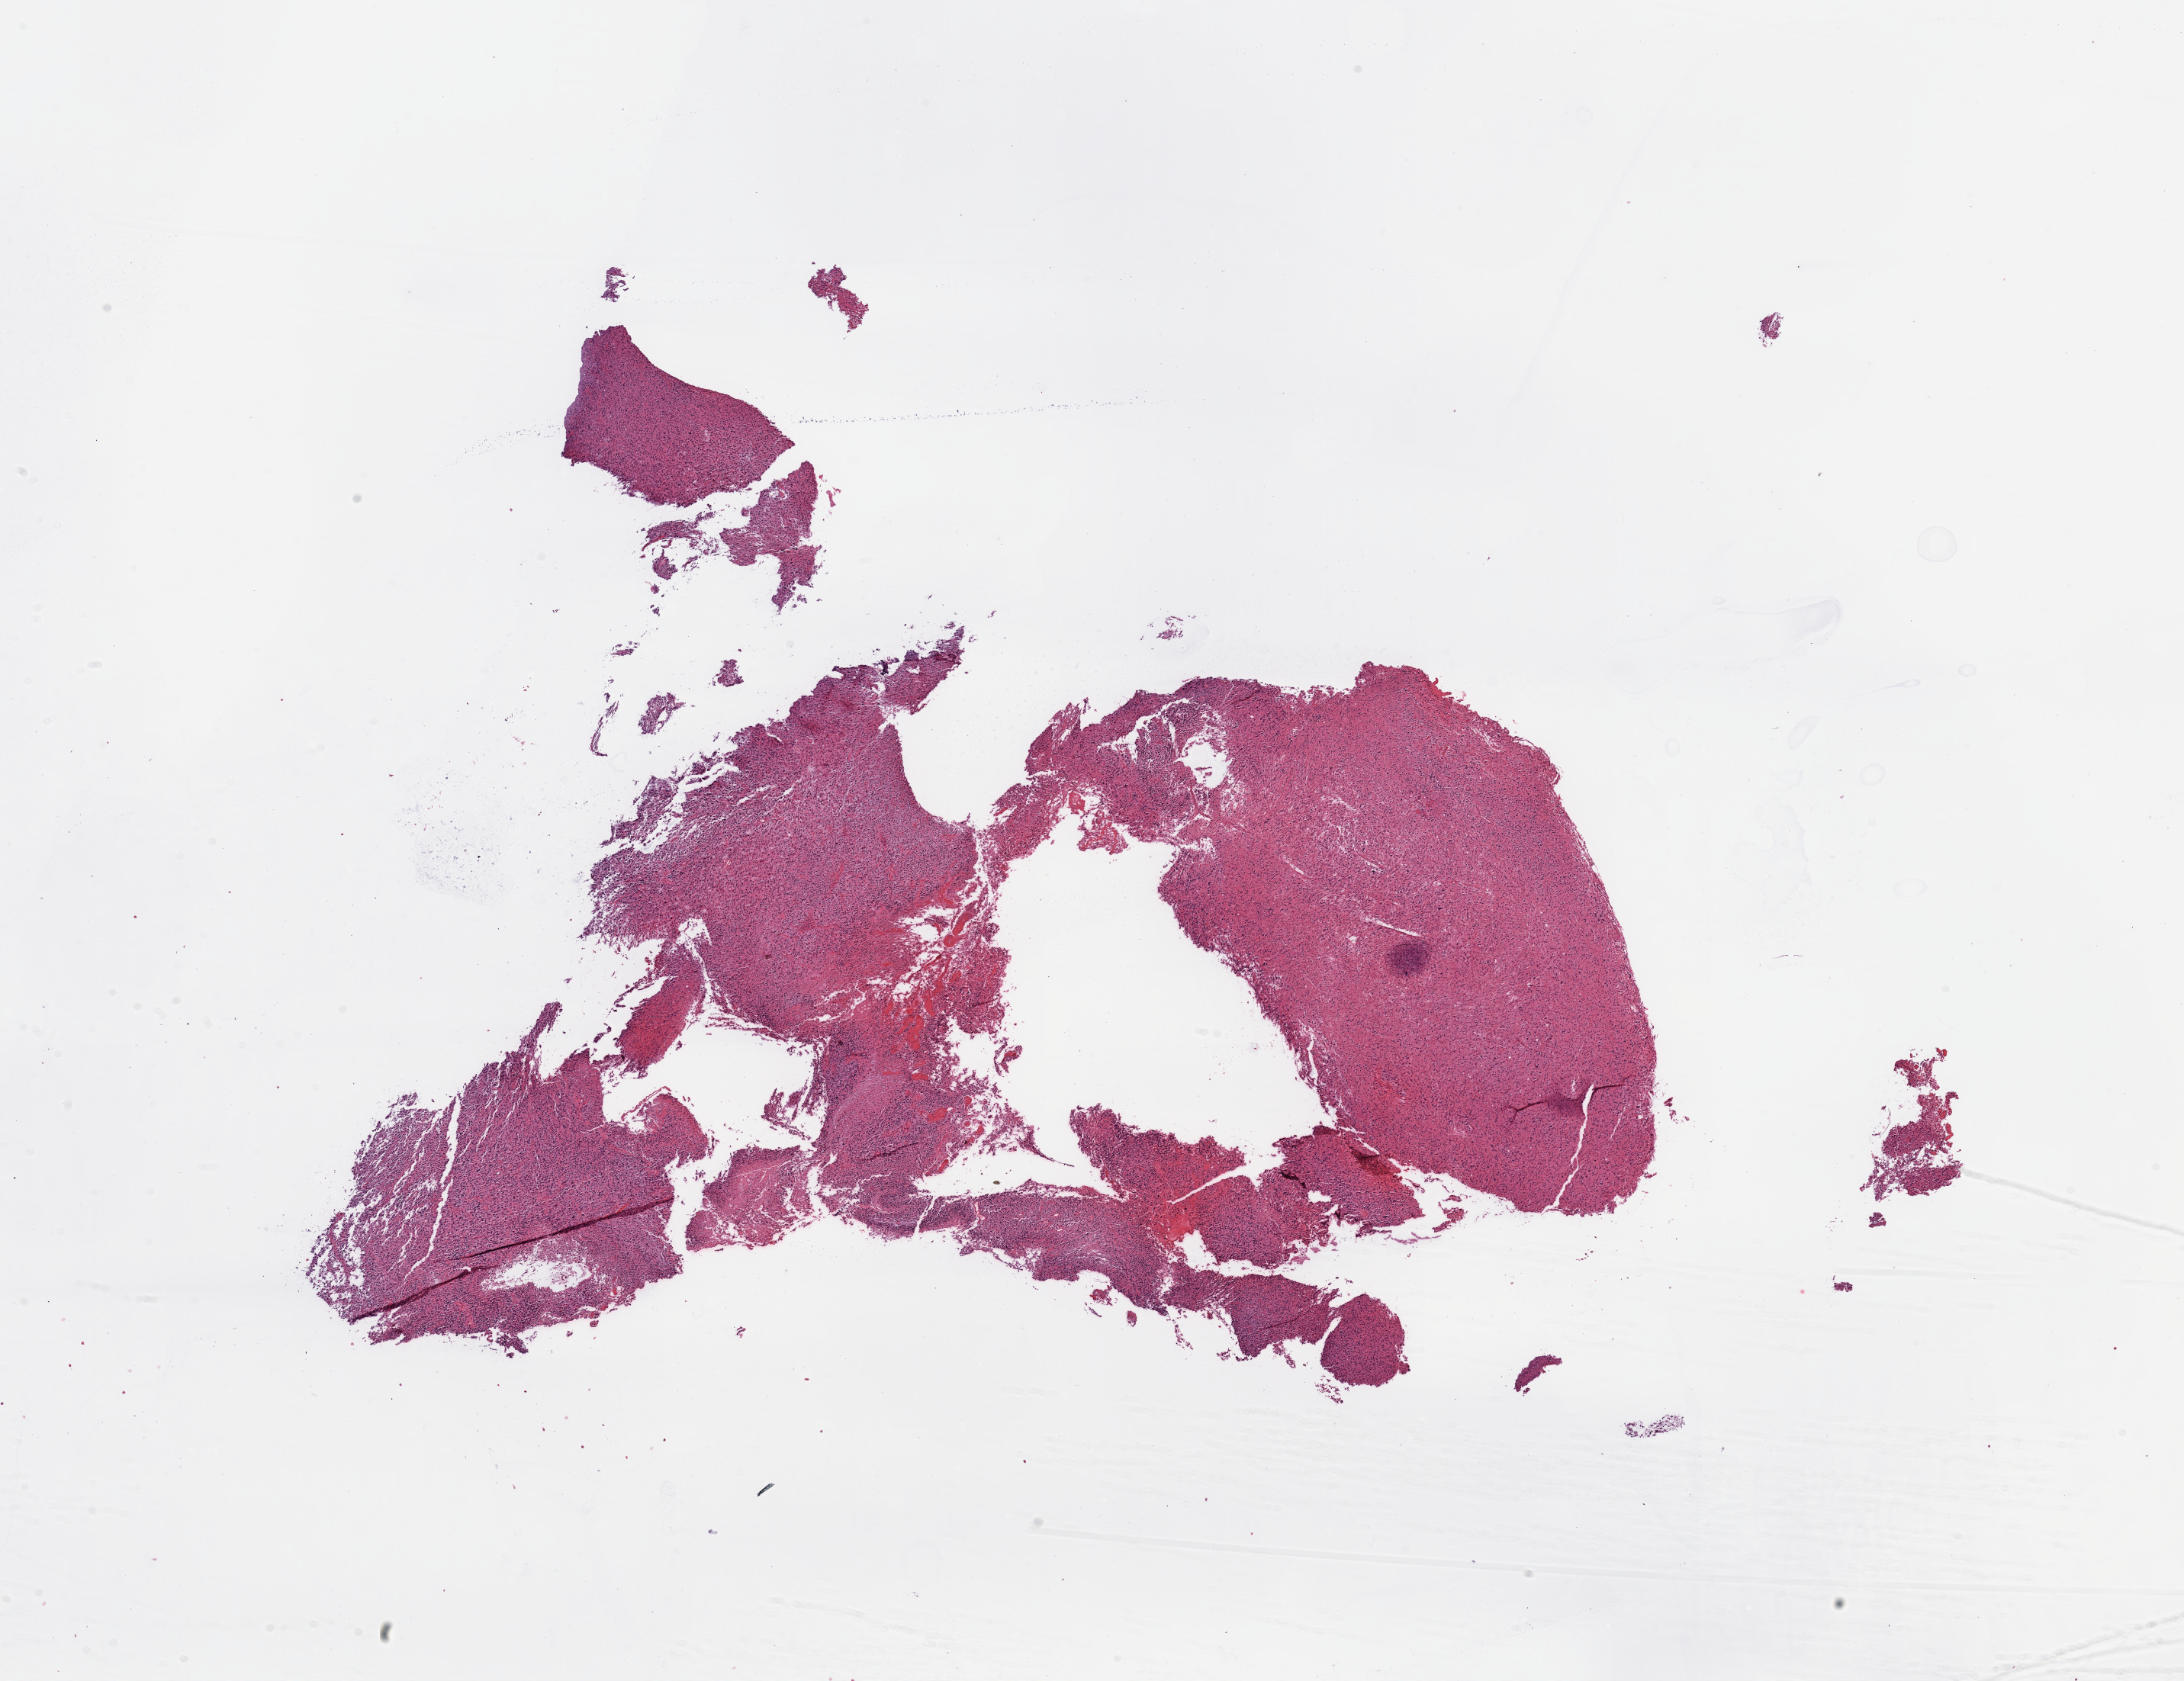
Digitized H&E tissue section (whole slide), a low-resolution overview of the entire scanned area, about 22.6 x 17.4 mm (from a 20x scan); brain, tumour tissue. Male, 70 y/o.
- patient diagnosis (cohort enrolment): glioblastoma multiforme (brain)
- primary tumour site (as recorded): parietal lobe